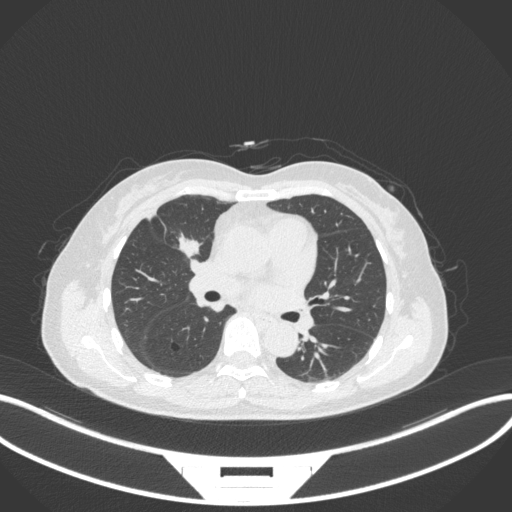
Chest CT, one axial slice; position 164 of 282 along the scan axis; lung window (W 1500 / L -600 HU); 1 mm slice thickness; 512 × 512 image matrix. Patient: female, 51 years. From the clinical record (not read from this slice): clinical TNM (as recorded): T1c N0 M0; histopathological grade: G2.
Outlined on this slice (rectangle marked by the reading radiologist):
- lung tumour (recorded histology: adenocarcinoma): box from (x=173, y=228) to (x=202, y=258) px